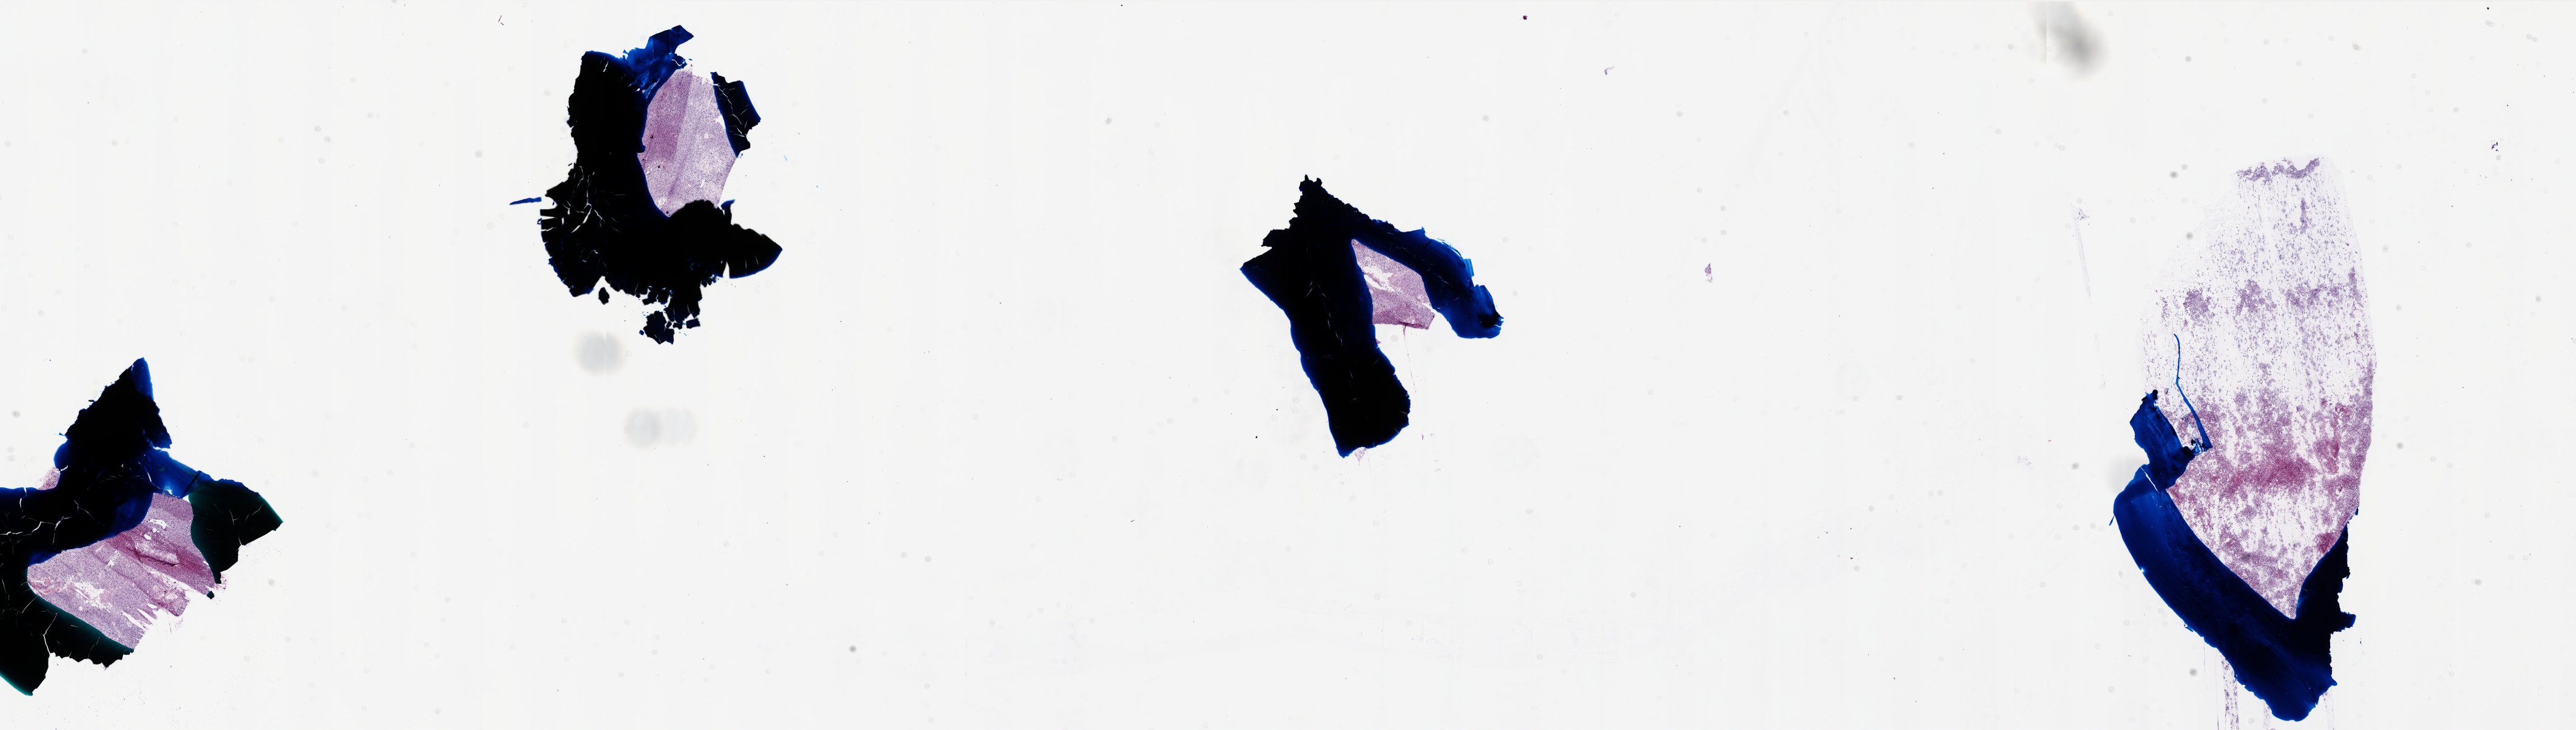
Digitized H&E tissue section (whole slide) — a low-resolution overview of the entire scanned area, about 34.0 x 9.6 mm (acquisition: 20x scan). Frozen section from the top of the tissue portion. Sample: primary tumour, brain. Female patient; age at initial diagnosis 72 years. Slide review estimates, as recorded: tumour cells 85%, tumour nuclei 95%, normal cells 0%, stromal cells 5%, necrosis 10%.
Pathologic diagnosis: Glioblastoma.